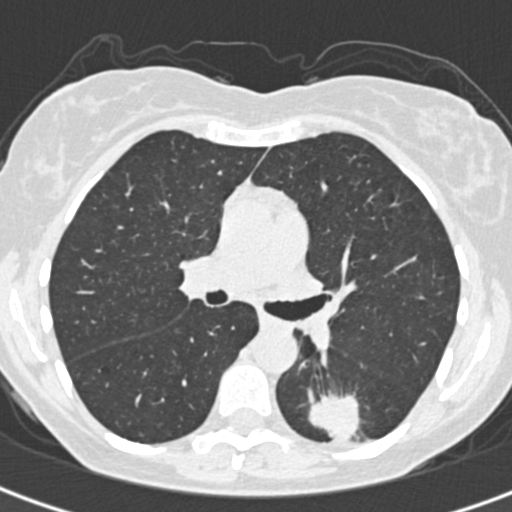
Low-dose screening chest CT, one axial slice. Slice 201 of 328 in the series (ordered by position). 120 kVp. Lung window (W 1500 / L -600 HU). 1 mm slice thickness. 512 × 512 image matrix, field of view 284 × 284 mm.
Structures marked on this image (expert manual segmentation):
- lesion 1 (tumor, lower lobe of left lung): bounding box [x1, y1, x2, y2] px = [308, 393, 361, 441]